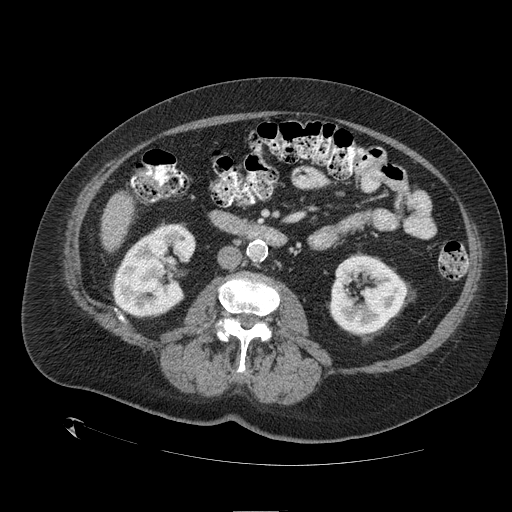
Contrast-enhanced abdominal CT (liver protocol), one axial slice; reconstruction kernel STANDARD; one of 2 acquisitions stored at this slice position; soft-tissue window (W 400 / L 40 HU); 2.5 mm slice thickness; 512 × 512 image matrix. From the clinical record (not read from this slice): diagnosis: hepatocellular carcinoma (patient treated with transarterial chemoembolisation; whether this scan precedes or follows treatment is not stated here); TNM stage (as recorded): Stage-I; Child-Pugh class: A; tumour differentiation: no biopsy; tumour nodularity: uninodular.
Annotated regions visible in this slice (semi-automatically segmented with operator editing):
- liver parenchyma outside the tumour (the mass and vessels are separate outlines, so this box may not span the whole liver): bounding box <101,192,132,250> (left, top, right, bottom; pixels)